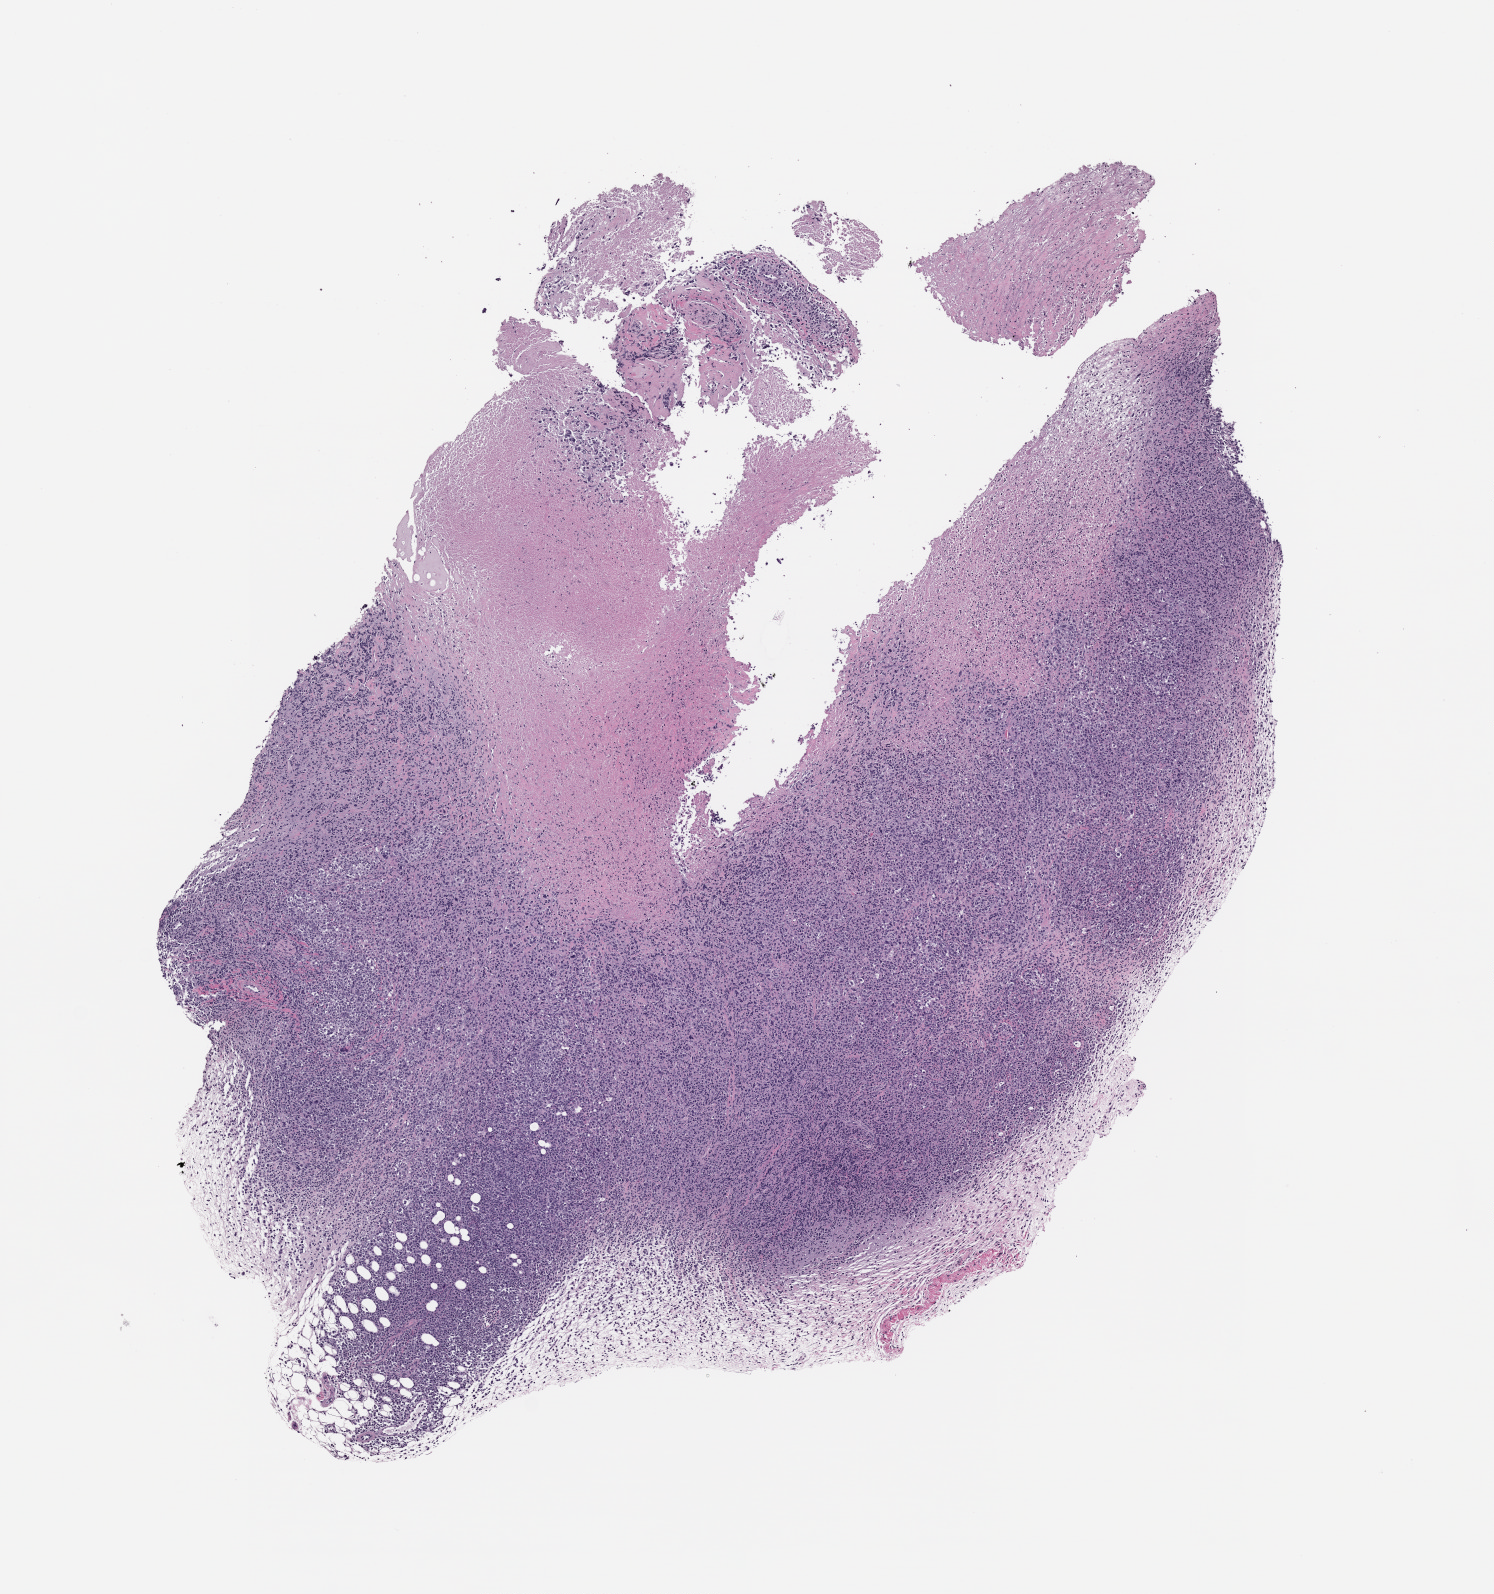
Haematoxylin and eosin whole-slide image of a patient-derived xenograft (PDX) tumor grown in a mouse, a low-resolution overview of the entire scanned area, about 6.0 x 6.4 mm.
• specimen: formalin-fixed, paraffin-embedded (FFPE) tissue